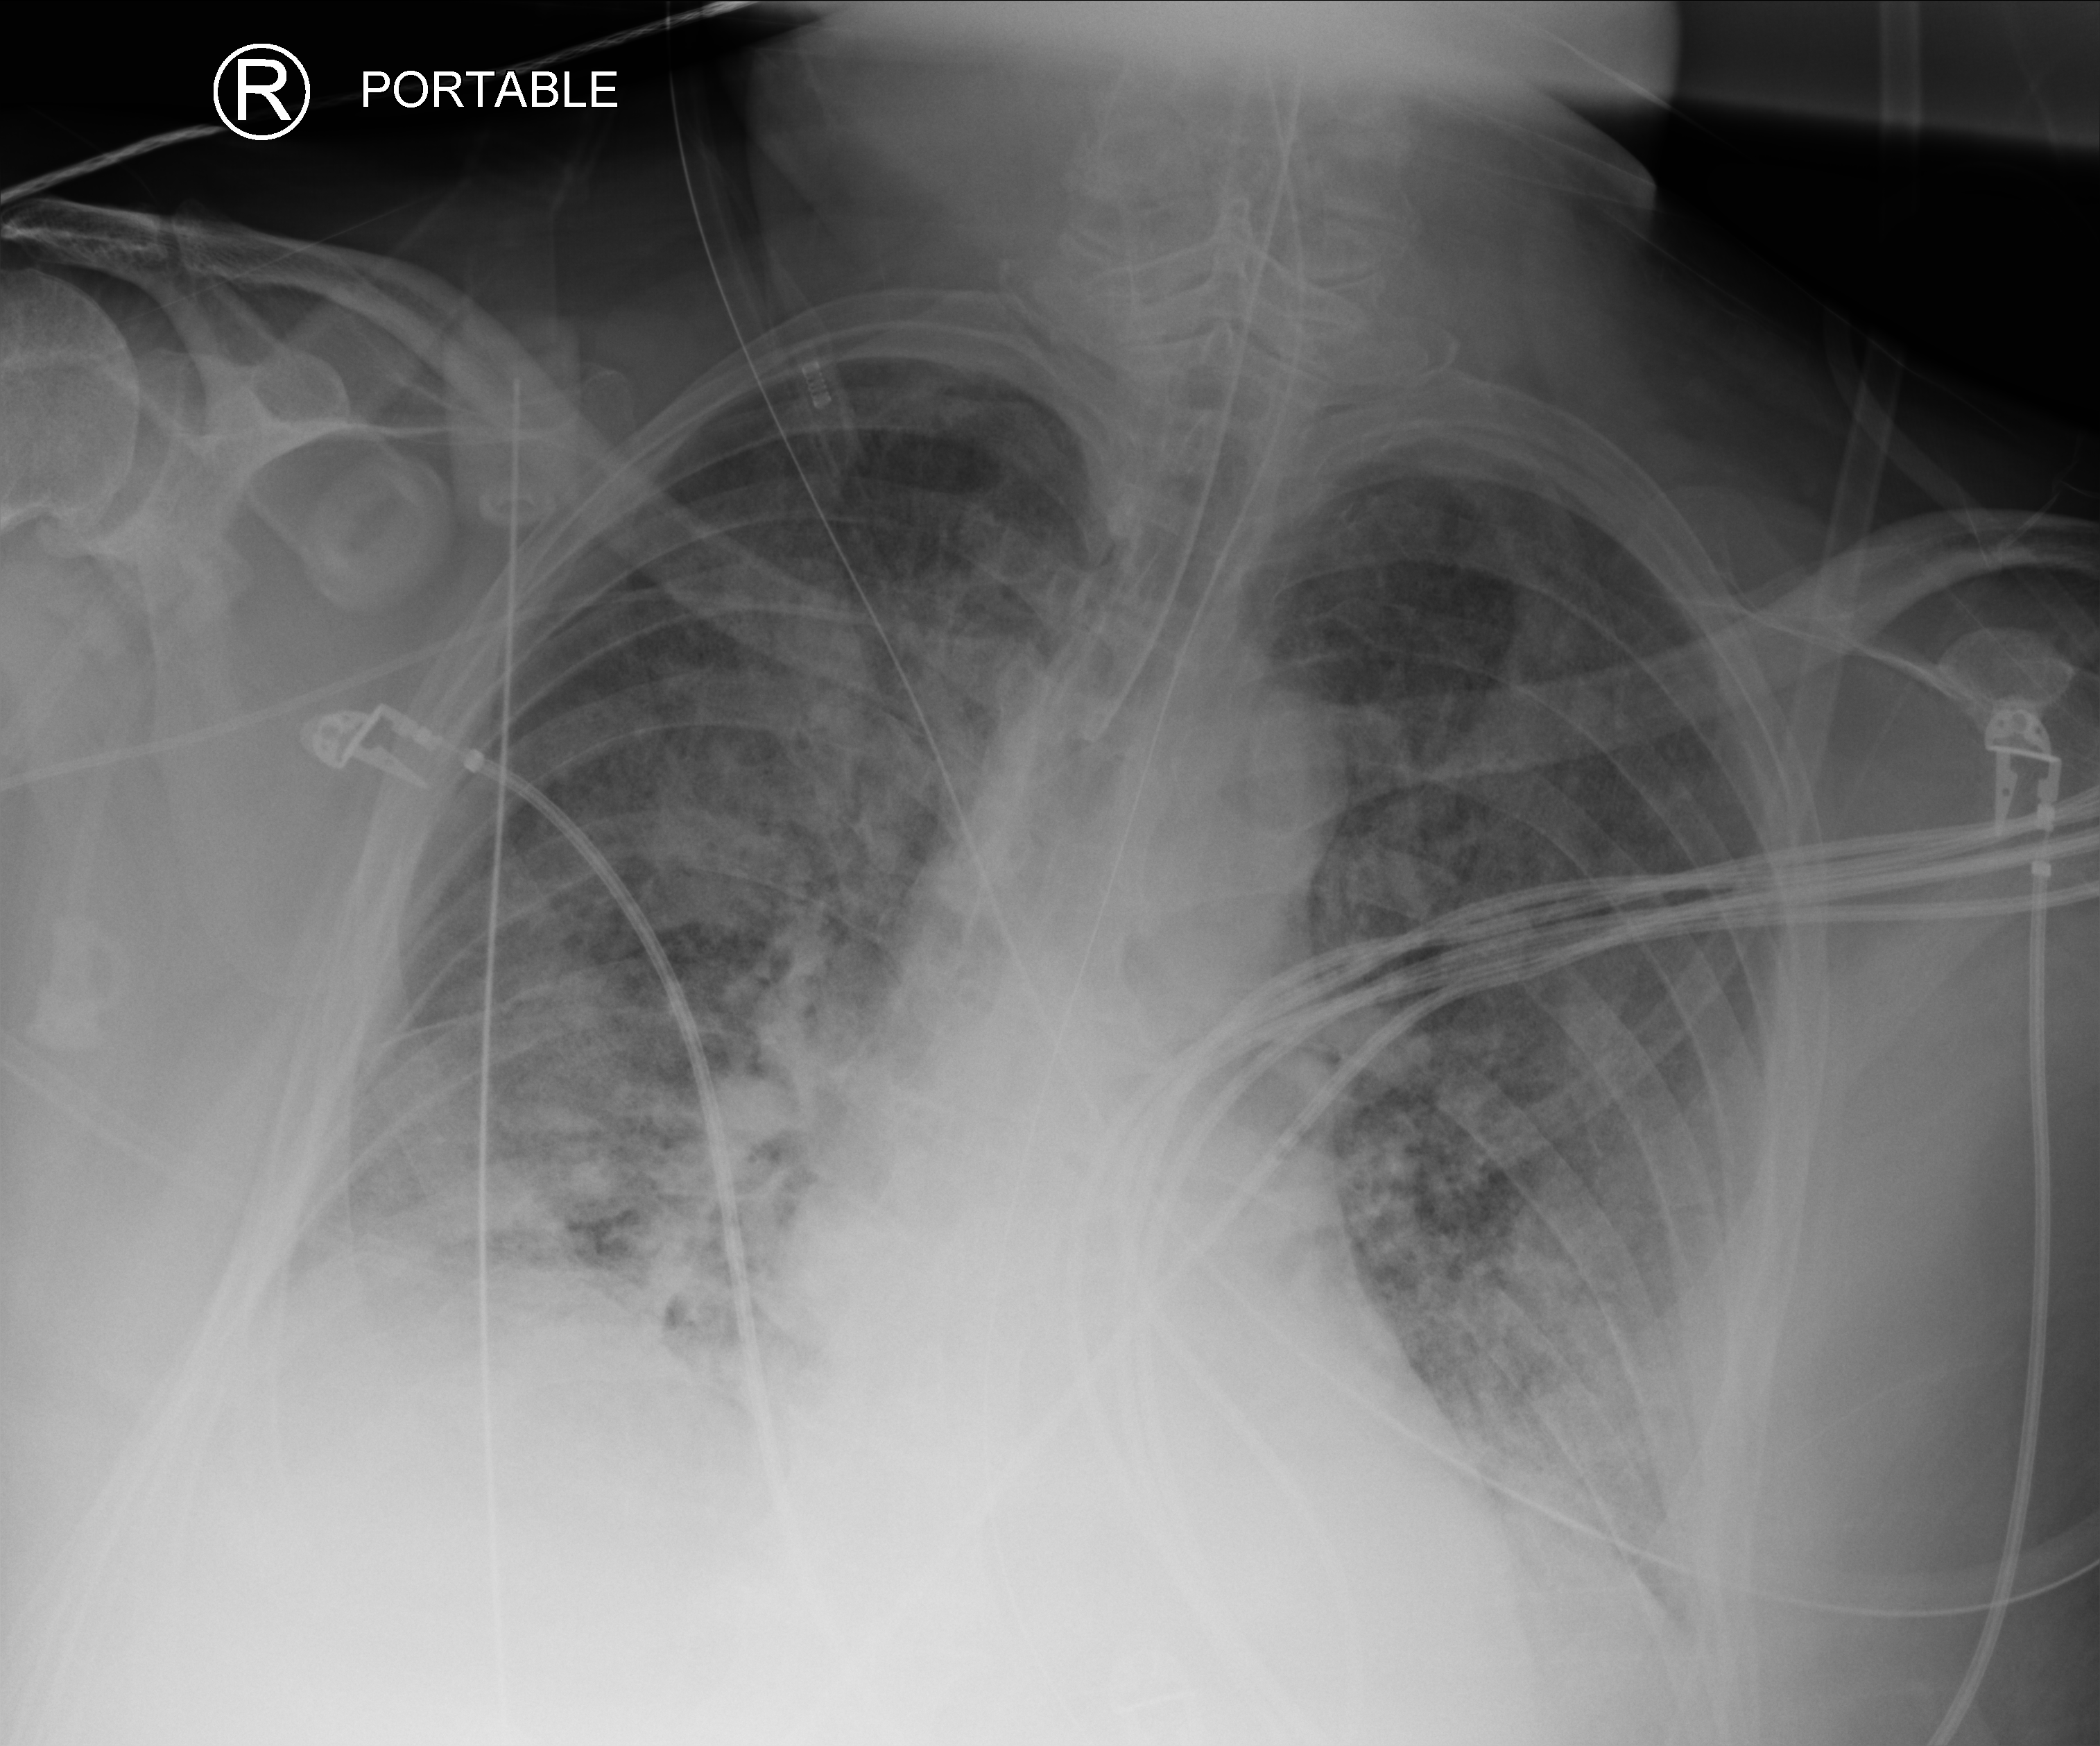
Portable chest radiograph, anteroposterior (AP) projection. Patient hospitalised with COVID-19; male, aged 60–74 years.
From the hospital-stay record, not from the radiograph (when in the stay this image was taken is not recorded):
- chronic kidney disease (admission record): no
- admitted to intensive care during this hospital stay: yes
- mechanically ventilated during this hospital stay: yes